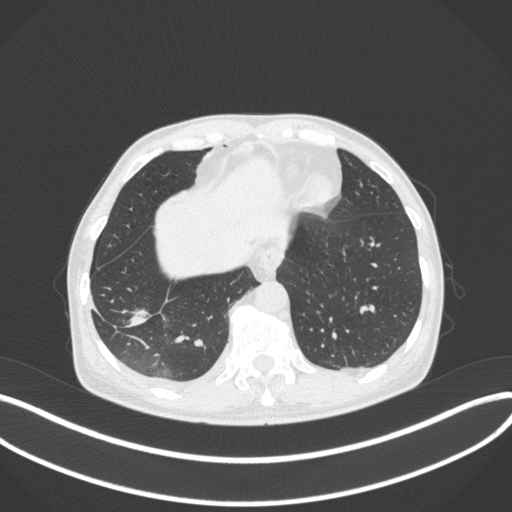
Chest CT, one axial slice; position 82 of 385 along the scan axis; lung window (W 1500 / L -600 HU); 1 mm slice thickness; 512 × 512 image matrix. Patient: male, 64 years. Case-level facts recorded for this patient, not image findings: clinical TNM (as recorded): T3 N0 M0; histopathological grade: G2-3.
Structures marked on this image (bounding box drawn by a radiologist):
- lung tumour (recorded histology: adenocarcinoma): bounding box (x1, y1, x2, y2) in pixels: (123, 302, 150, 333)